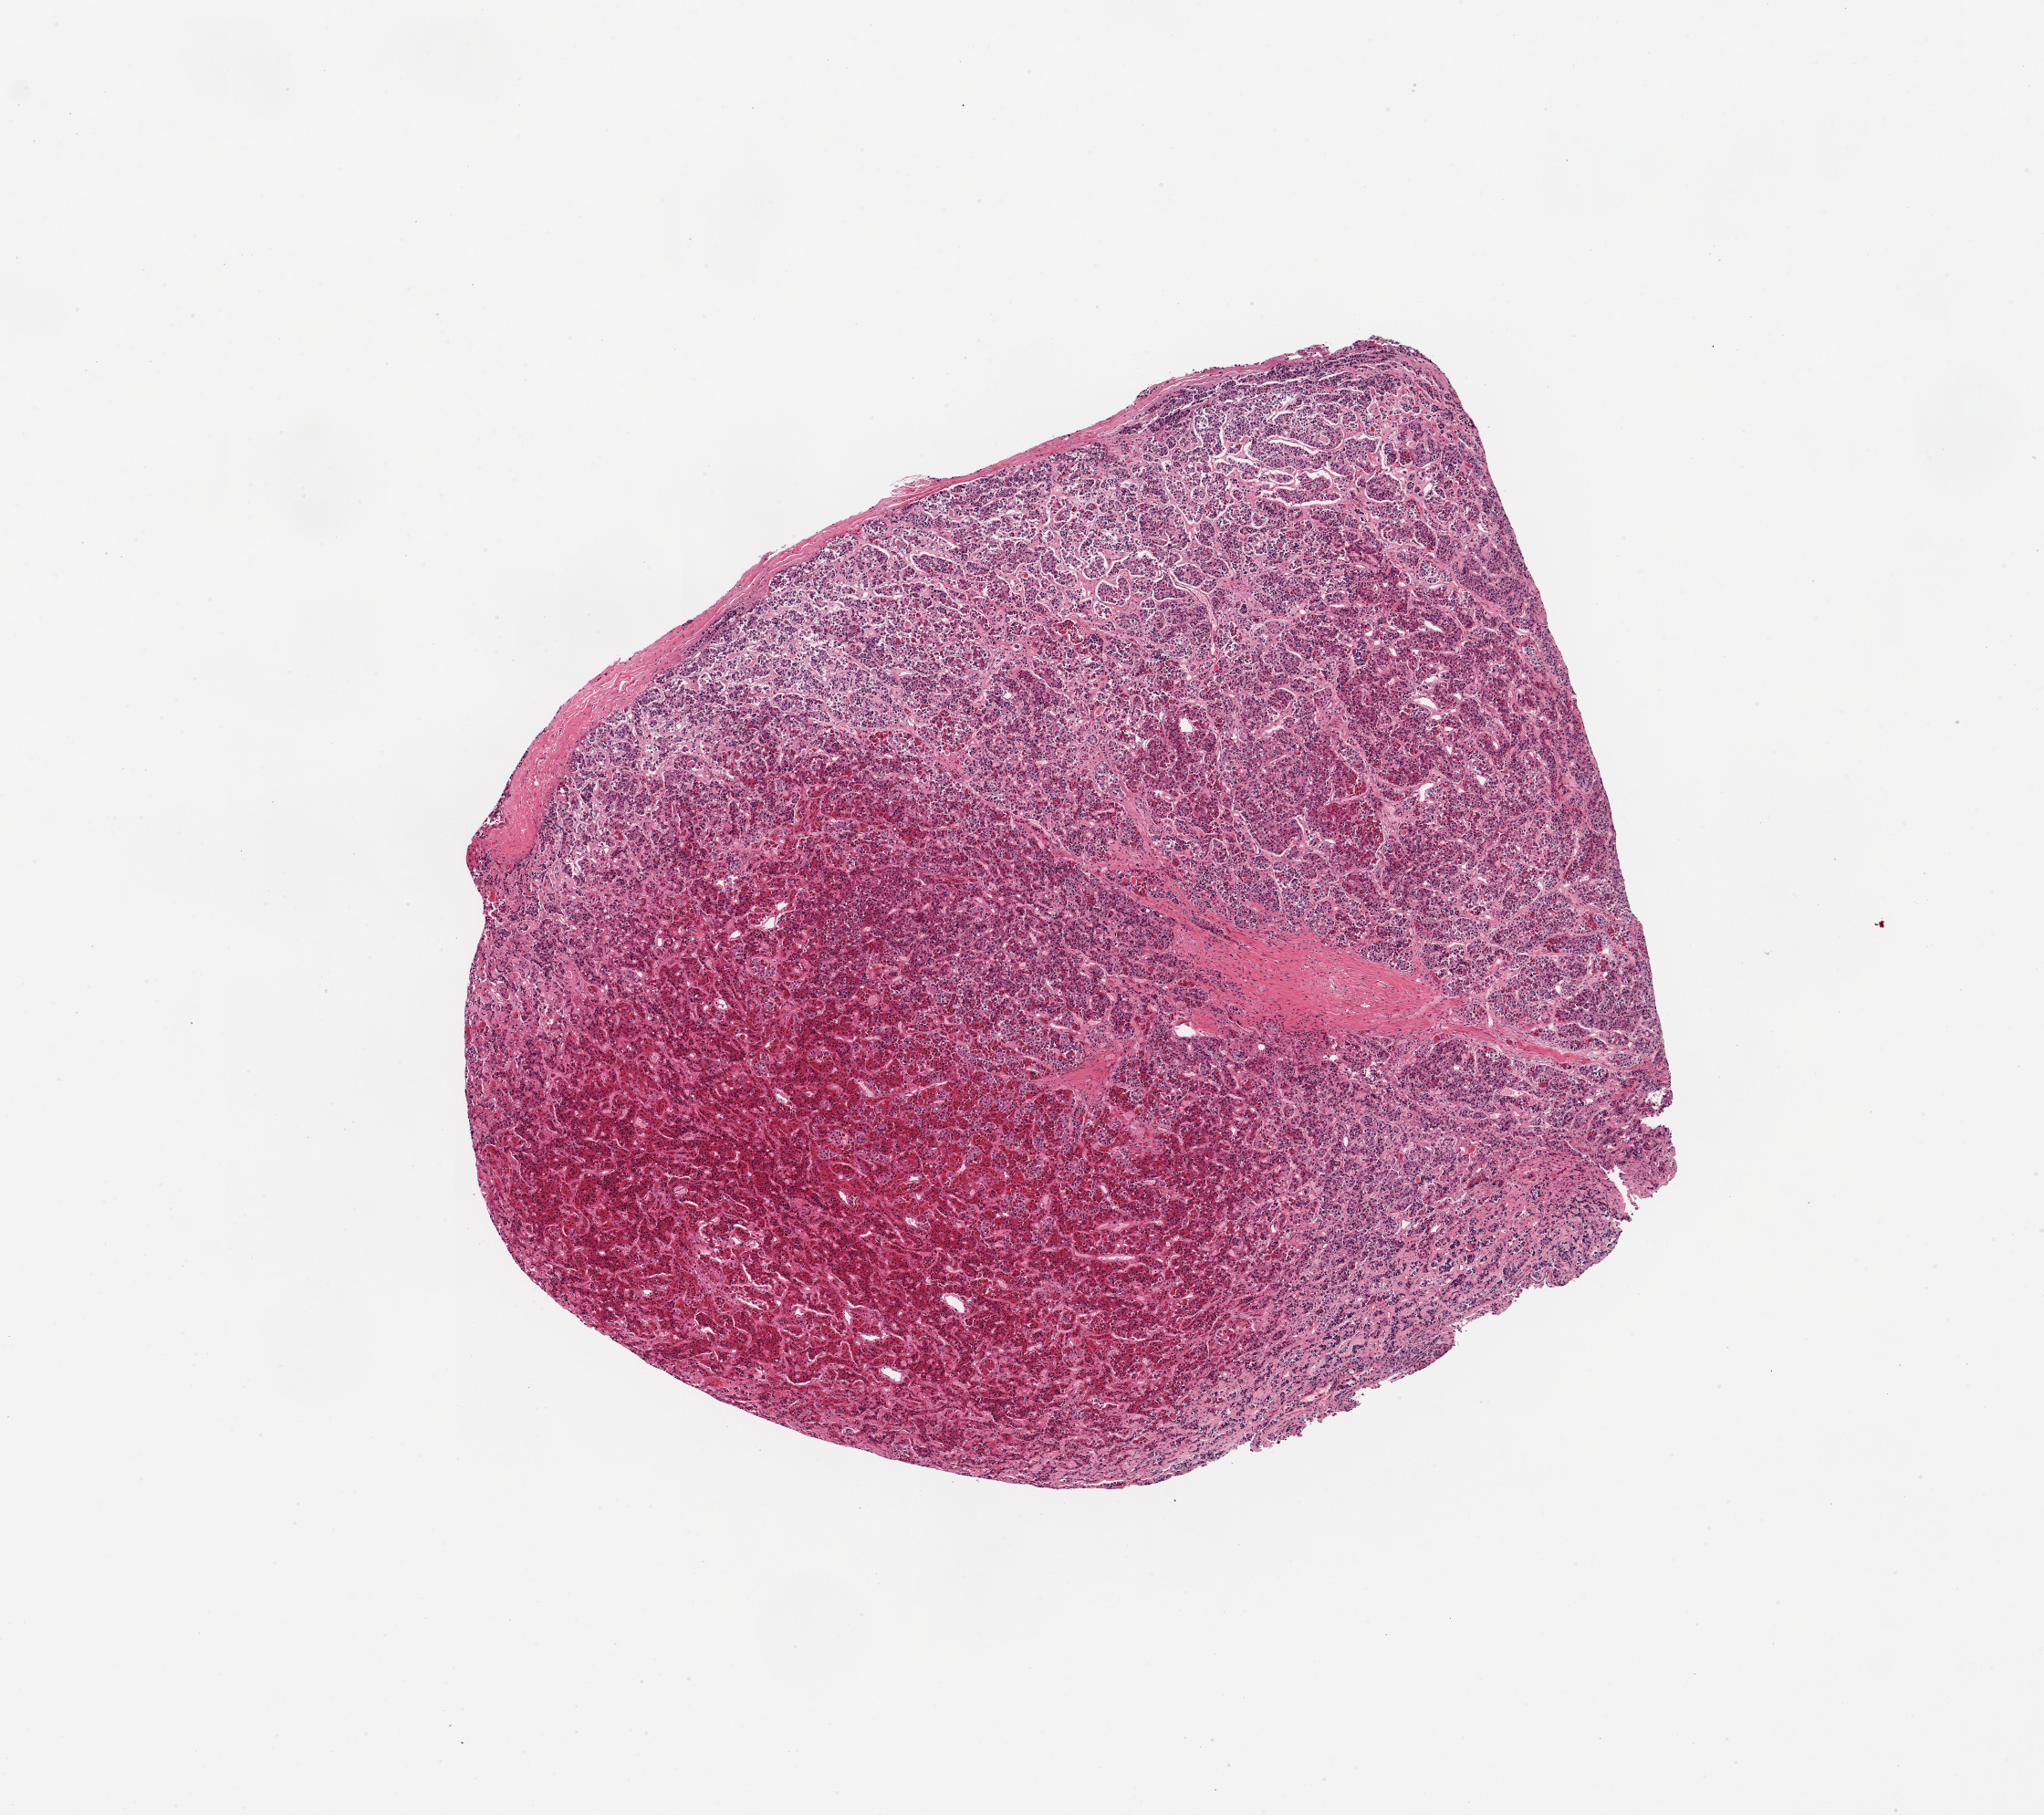
Whole-slide image, H&E stain, a low-resolution overview of the entire scanned area, about 8.9 x 7.9 mm (acquisition: 20x scan). PAXgene-fixed paraffin-embedded (PFPE) section. Target tissue: pituitary. Donor tissue sample.
Review note (as recorded): 1 piece; all anterior.